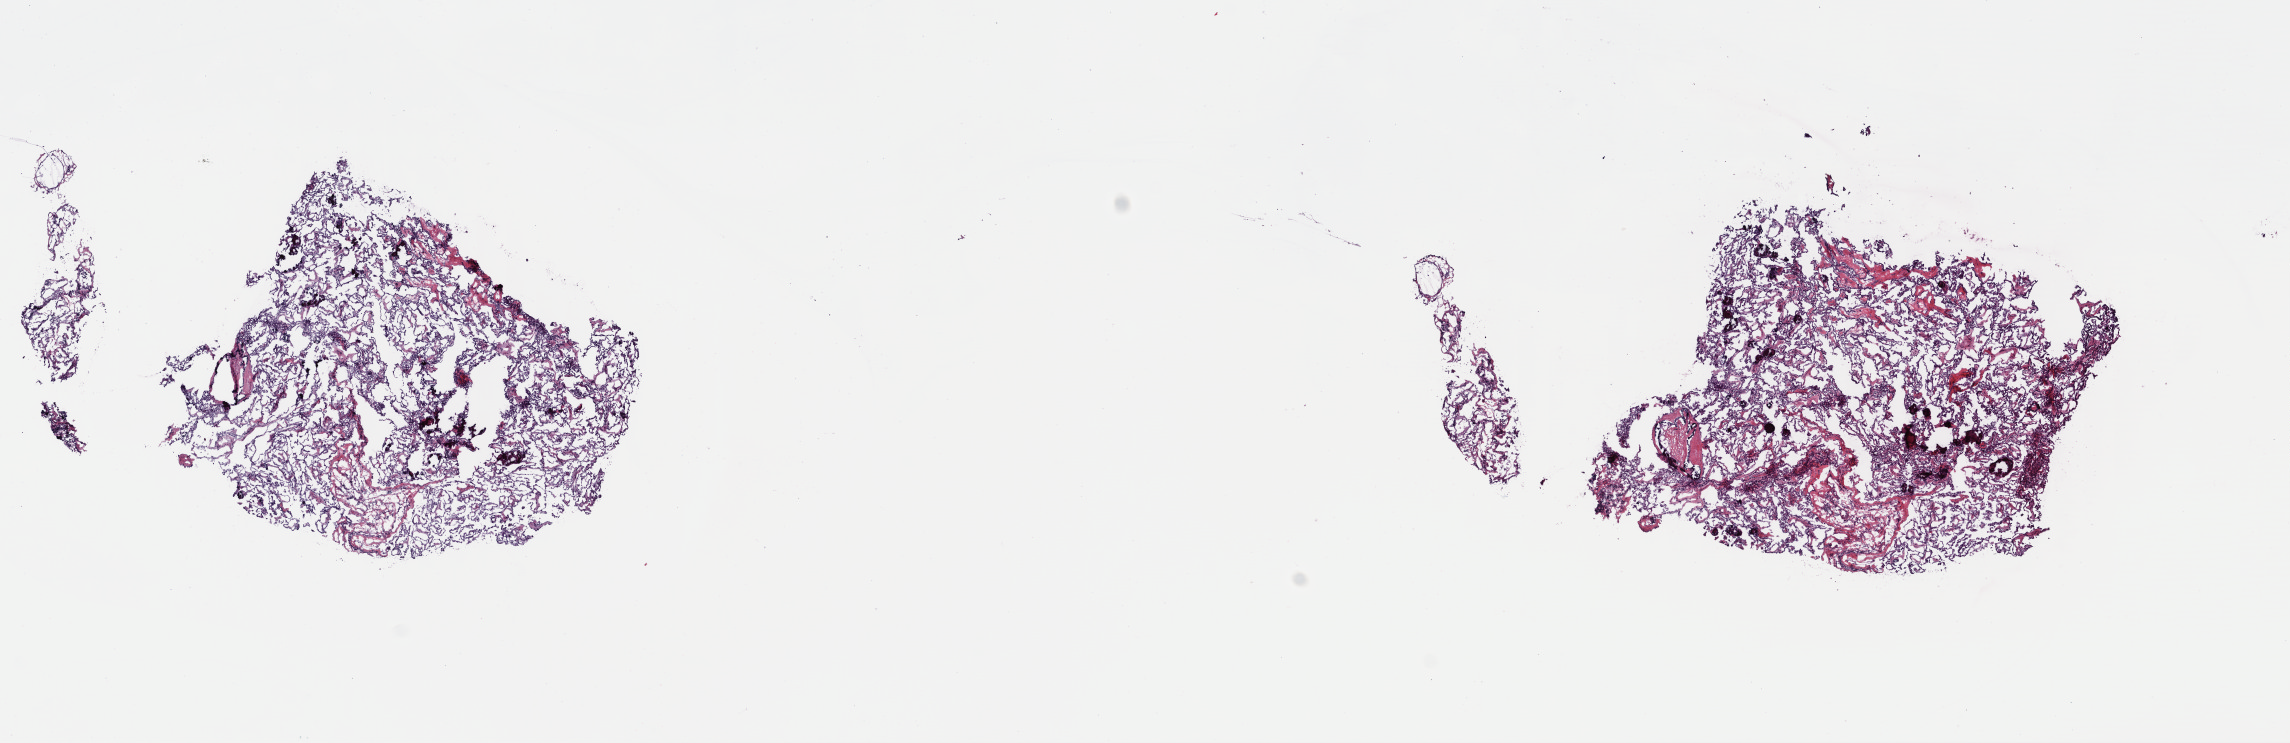
Whole-slide histology image, H&E, whole scanned area (about 18.0 x 5.8 mm) shown as a low-resolution overview. Frozen section from the top of the tissue portion. Primary tumour sample from the thyroid. Female, age 59 years at initial diagnosis.
Pathologic diagnosis: Papillary adenocarcinoma, NOS.